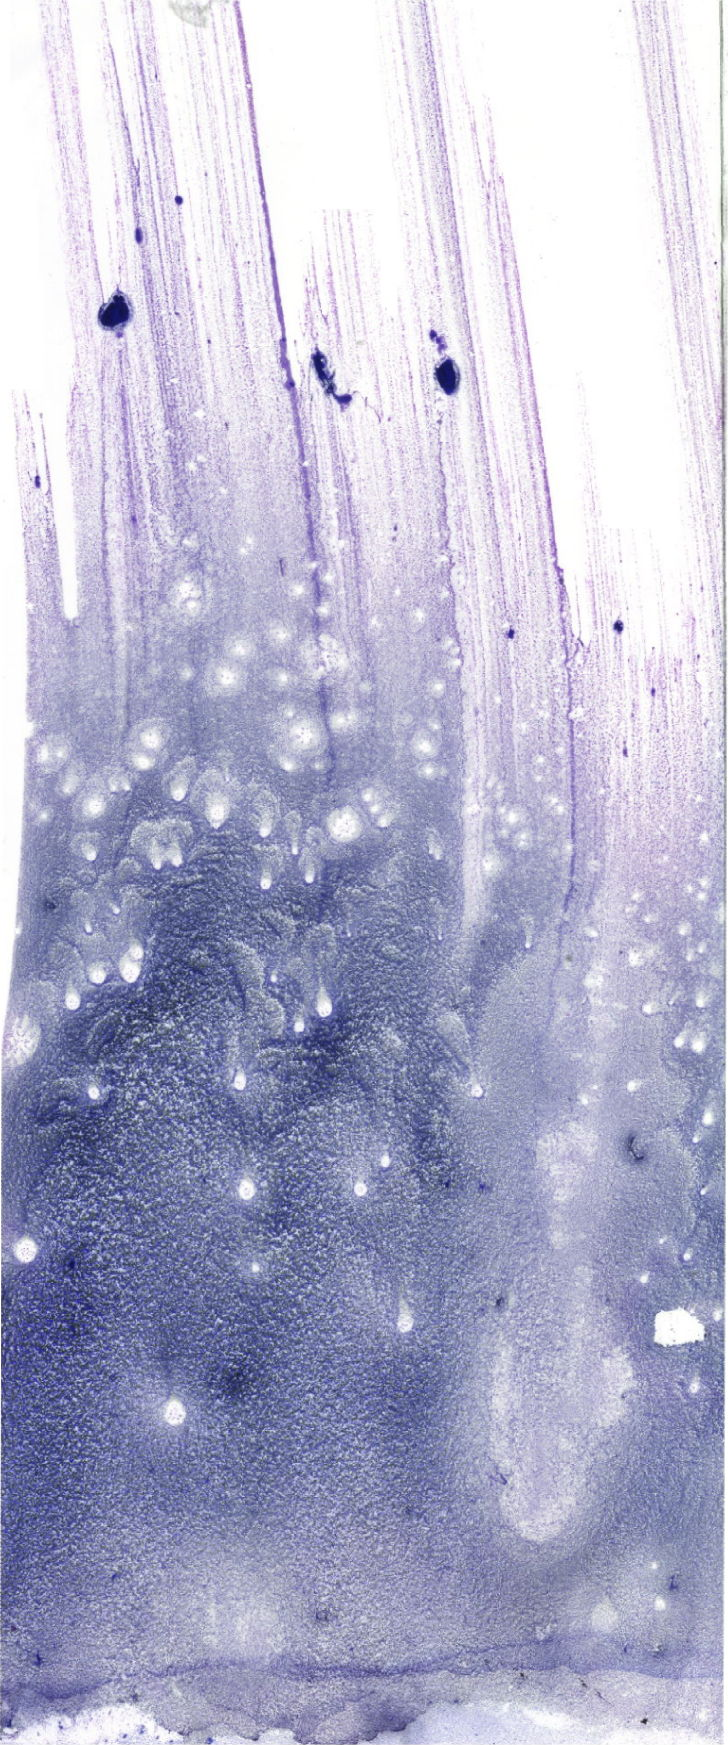
May-Grünwald-Giemsa (MGG)-stained marrow aspirate smear (whole slide) — low-resolution overview of the scanned area, about 20.6 x 49.5 mm. Female patient.
Diagnosis: B Acute Lymphoblastic Leukemia.